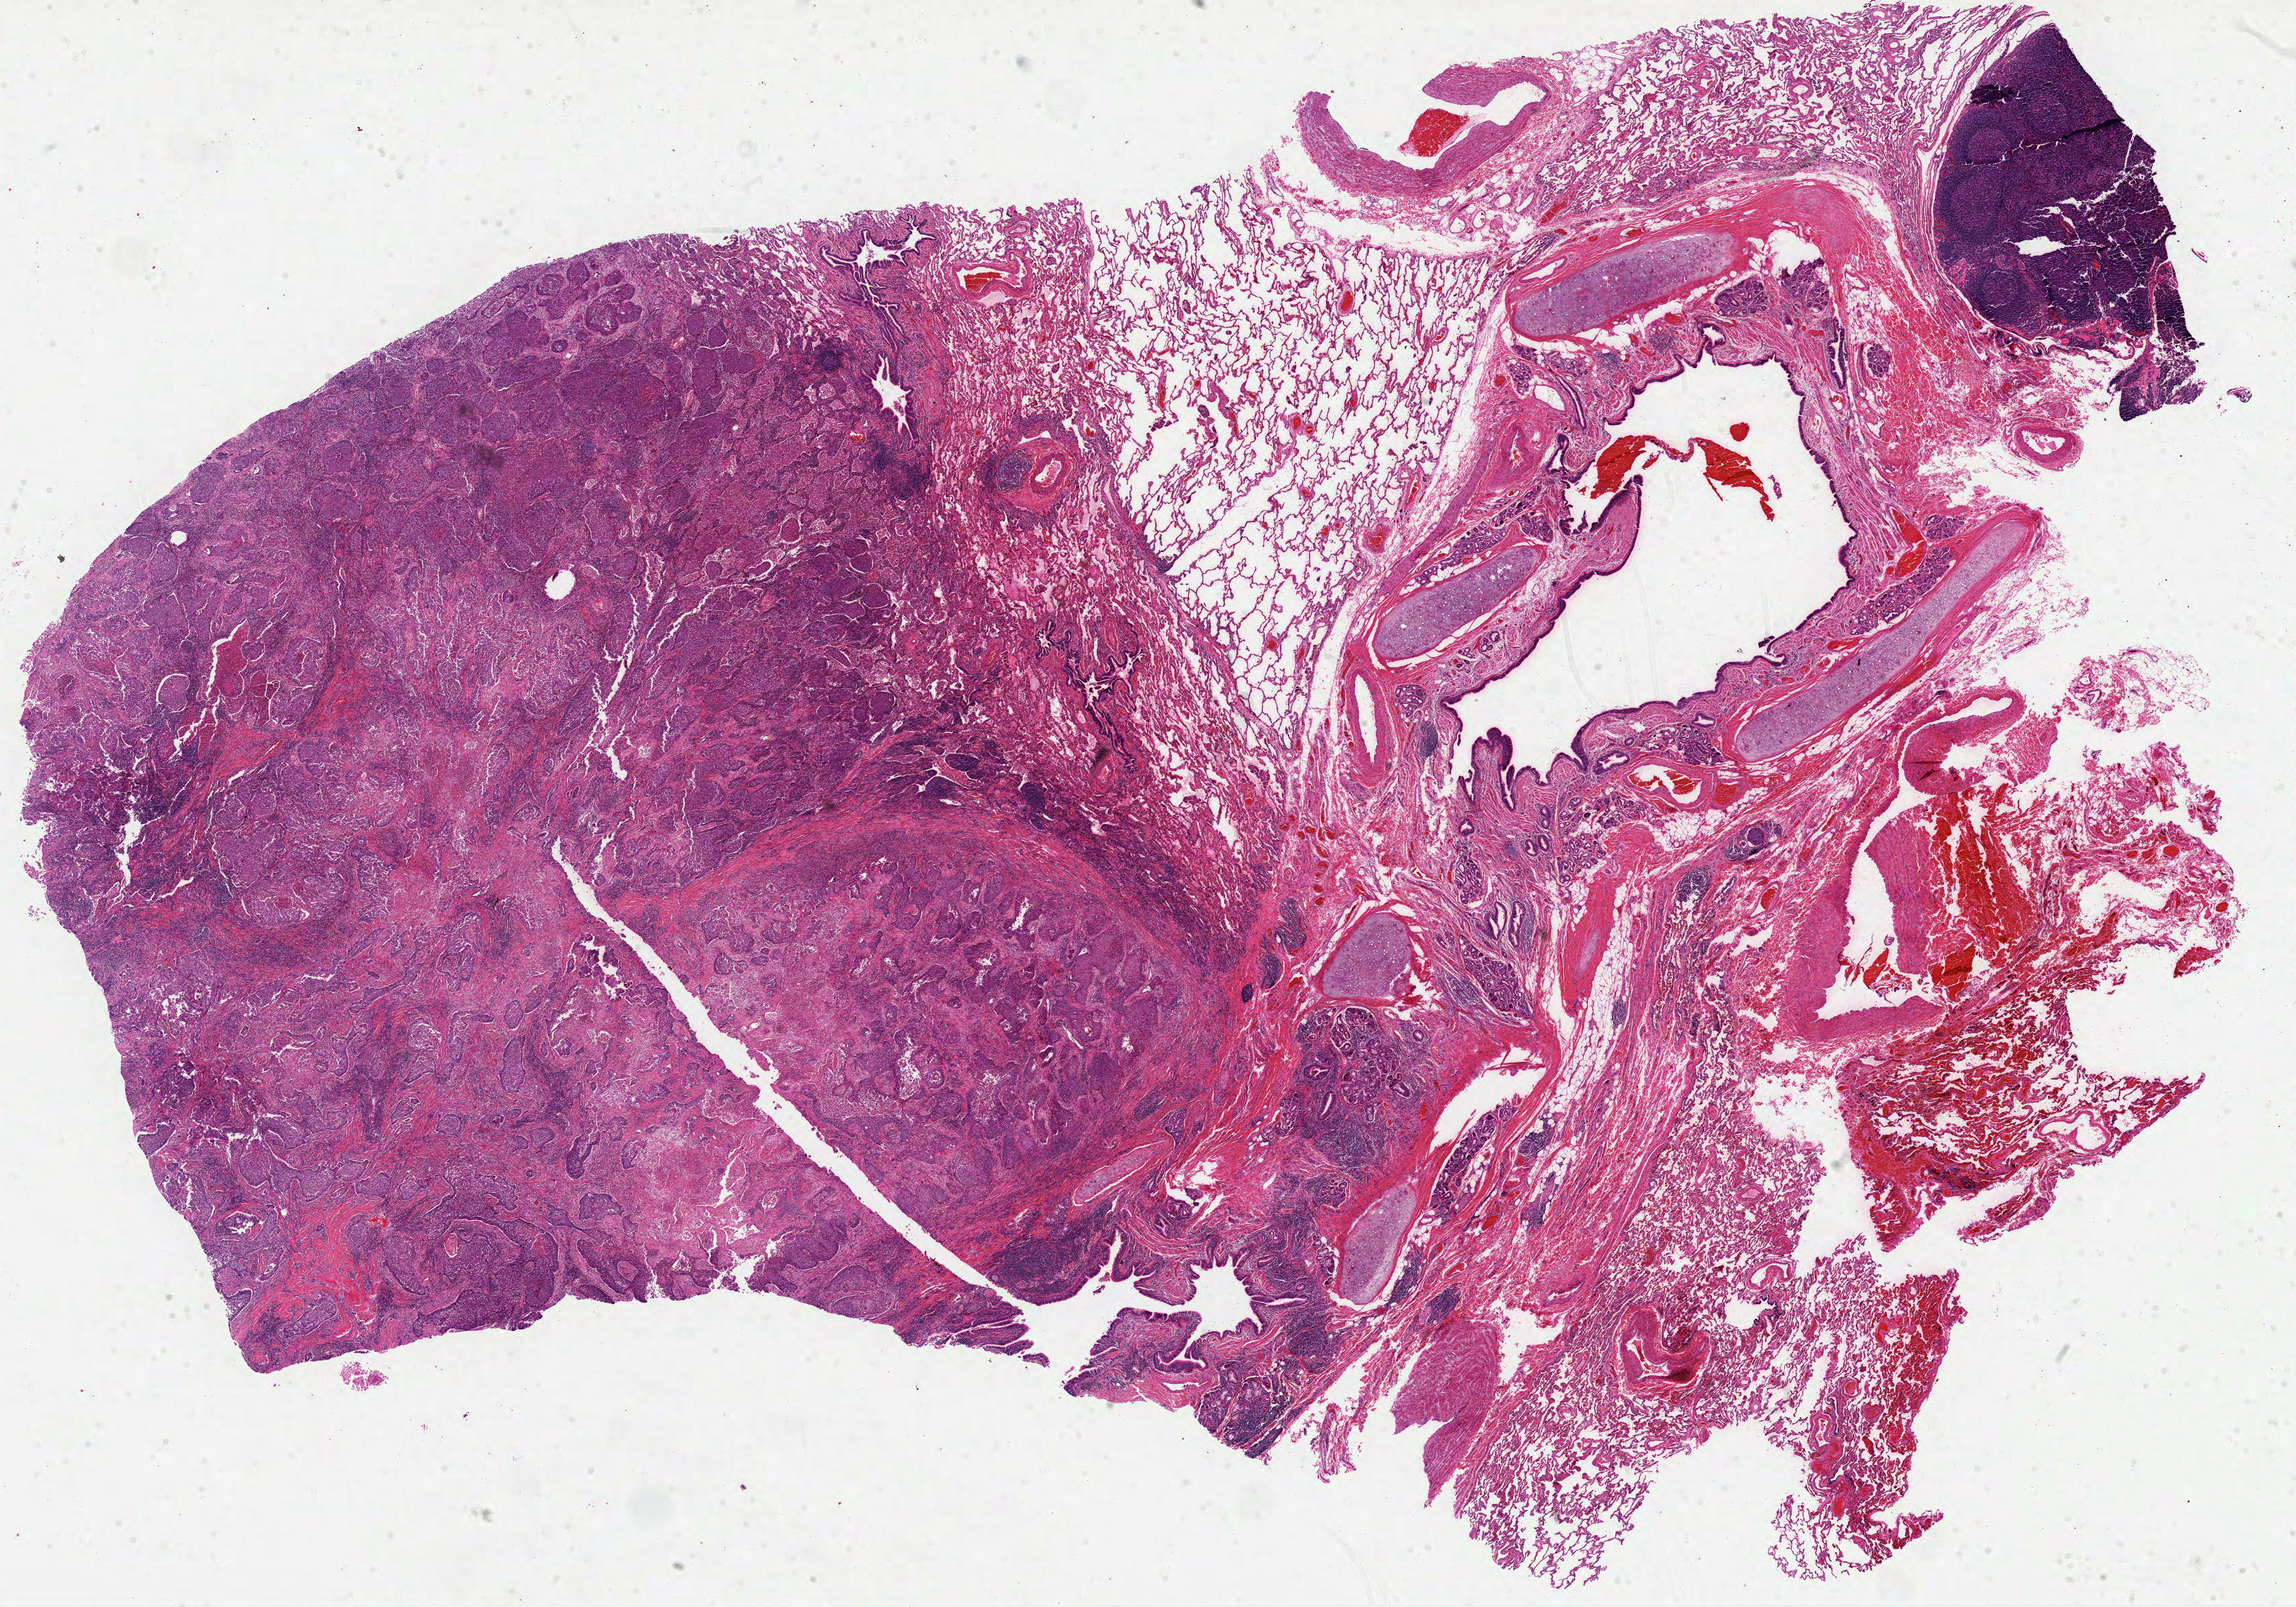
Digitized H&E-stained tissue section (whole slide) — a low-resolution overview of the entire scanned area, about 27.3 x 19.1 mm; formalin-fixed paraffin-embedded (FFPE) diagnostic section; sample: primary tumour, lung. Male, age 68 years at initial diagnosis.
Pathologic diagnosis: Squamous cell carcinoma, NOS.